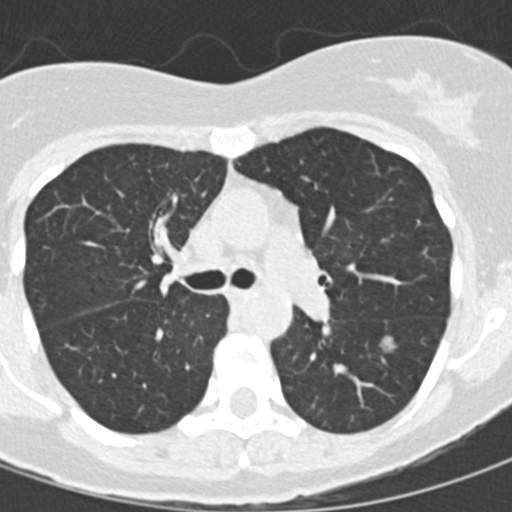
Low-dose screening chest CT, one axial slice; position 93 of 145 along the scan axis; reconstruction kernel B30f; 120 kVp; lung window (W 1500 / L -600 HU); 512 × 512 image matrix, field of view 270 × 270 mm.
Annotated regions visible in this slice (outlined manually by an expert reader):
- lesion 1 (tumor, lower lobe of left lung): bounding box <381,336,395,351> (left, top, right, bottom; pixels)